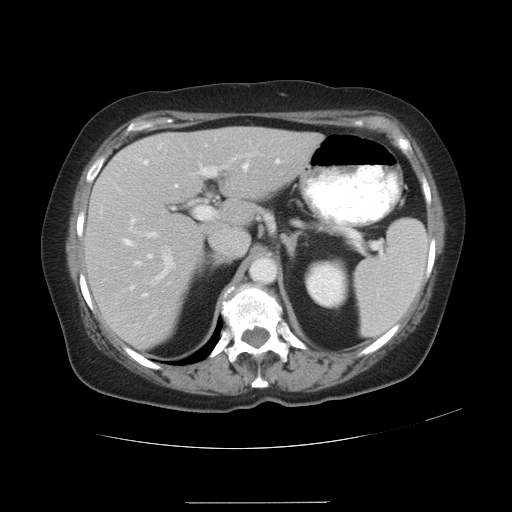
Contrast-enhanced abdominal CT, one axial slice. Position 19 of 32 along the scan axis. Reconstruction kernel STANDARD. 120 kVp. Intravenous contrast given. Soft-tissue window (W 400 / L 40 HU). 512 × 512 image matrix, field of view 386 × 386 mm. Female patient, age 65 years. Case-level facts recorded for this patient, not image findings: diagnosis: colorectal cancer liver metastases, imaged before liver resection; multiple liver metastases: yes; largest metastasis: 1.7 cm; disease in both lobes: no.
Annotated regions visible in this slice (manually delineated by an expert):
- liver: bounding box (x1, y1, x2, y2) in pixels: (87, 128, 318, 347)
- planned liver remnant (the part of the liver to remain after resection): (86, 133, 230, 346)
- portal vein (with intrahepatic branches): (122, 155, 249, 297)